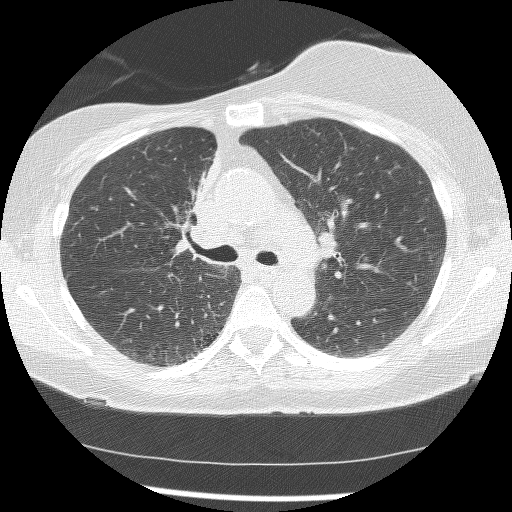
Low-dose screening chest CT, axial slice; baseline screening round; lung window (W 1500 / L -600 HU); slice 56 of 172 in the series; 512 × 512 image matrix. Female, age 56 years at enrolment.
- Lesion marked by an expert reader, bounding box [x1, y1, x2, y2] px = [162, 156, 218, 260].
- The screening reader recorded 2 non-calcified nodules or masses ≥4 mm on this exam; which of them this box marks is not recorded.
- Official screen result: positive, change unspecified: nodule(s) >= 4 mm or enlarging nodule(s), mass(es), or other non-specific abnormalities suspicious for lung cancer.
- Later outcome: lung cancer diagnosed 1185 days after this screen — adenocarcinoma, NOS, right upper lobe, stage IIIB (AJCC 6th edition), 8 mm at pathology.